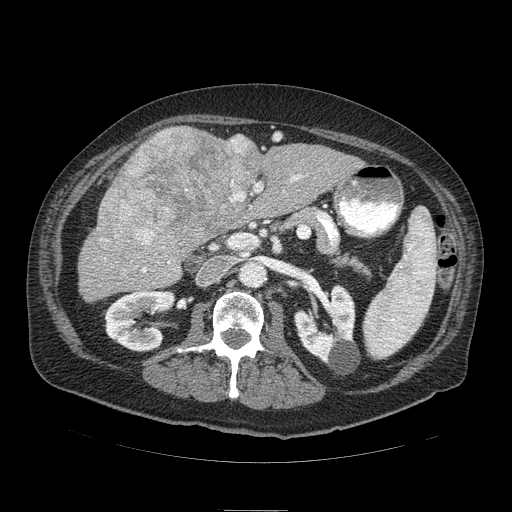
Contrast-enhanced abdominal CT (liver protocol), one axial slice. Position 39 of 103 along the scan axis. Reconstruction kernel STANDARD. 120 kVp. Soft-tissue window (W 400 / L 40 HU). 512 × 512 image matrix, field of view 440 × 440 mm. Case-level facts recorded for this patient, not image findings: diagnosis: hepatocellular carcinoma (patient treated with transarterial chemoembolisation; whether this scan precedes or follows treatment is not stated here); TNM stage (as recorded): Stage-IIIA; Child-Pugh class: B; tumour nodularity: multinodular.
Structures marked on this image (semi-automatically segmented with operator editing):
- liver parenchyma outside the tumour (the mass and vessels are separate outlines, so this box may not span the whole liver): bounding box [x1, y1, x2, y2] px = [78, 126, 364, 300]
- mass: [96, 126, 260, 258]
- liver vessels: [142, 175, 302, 272]